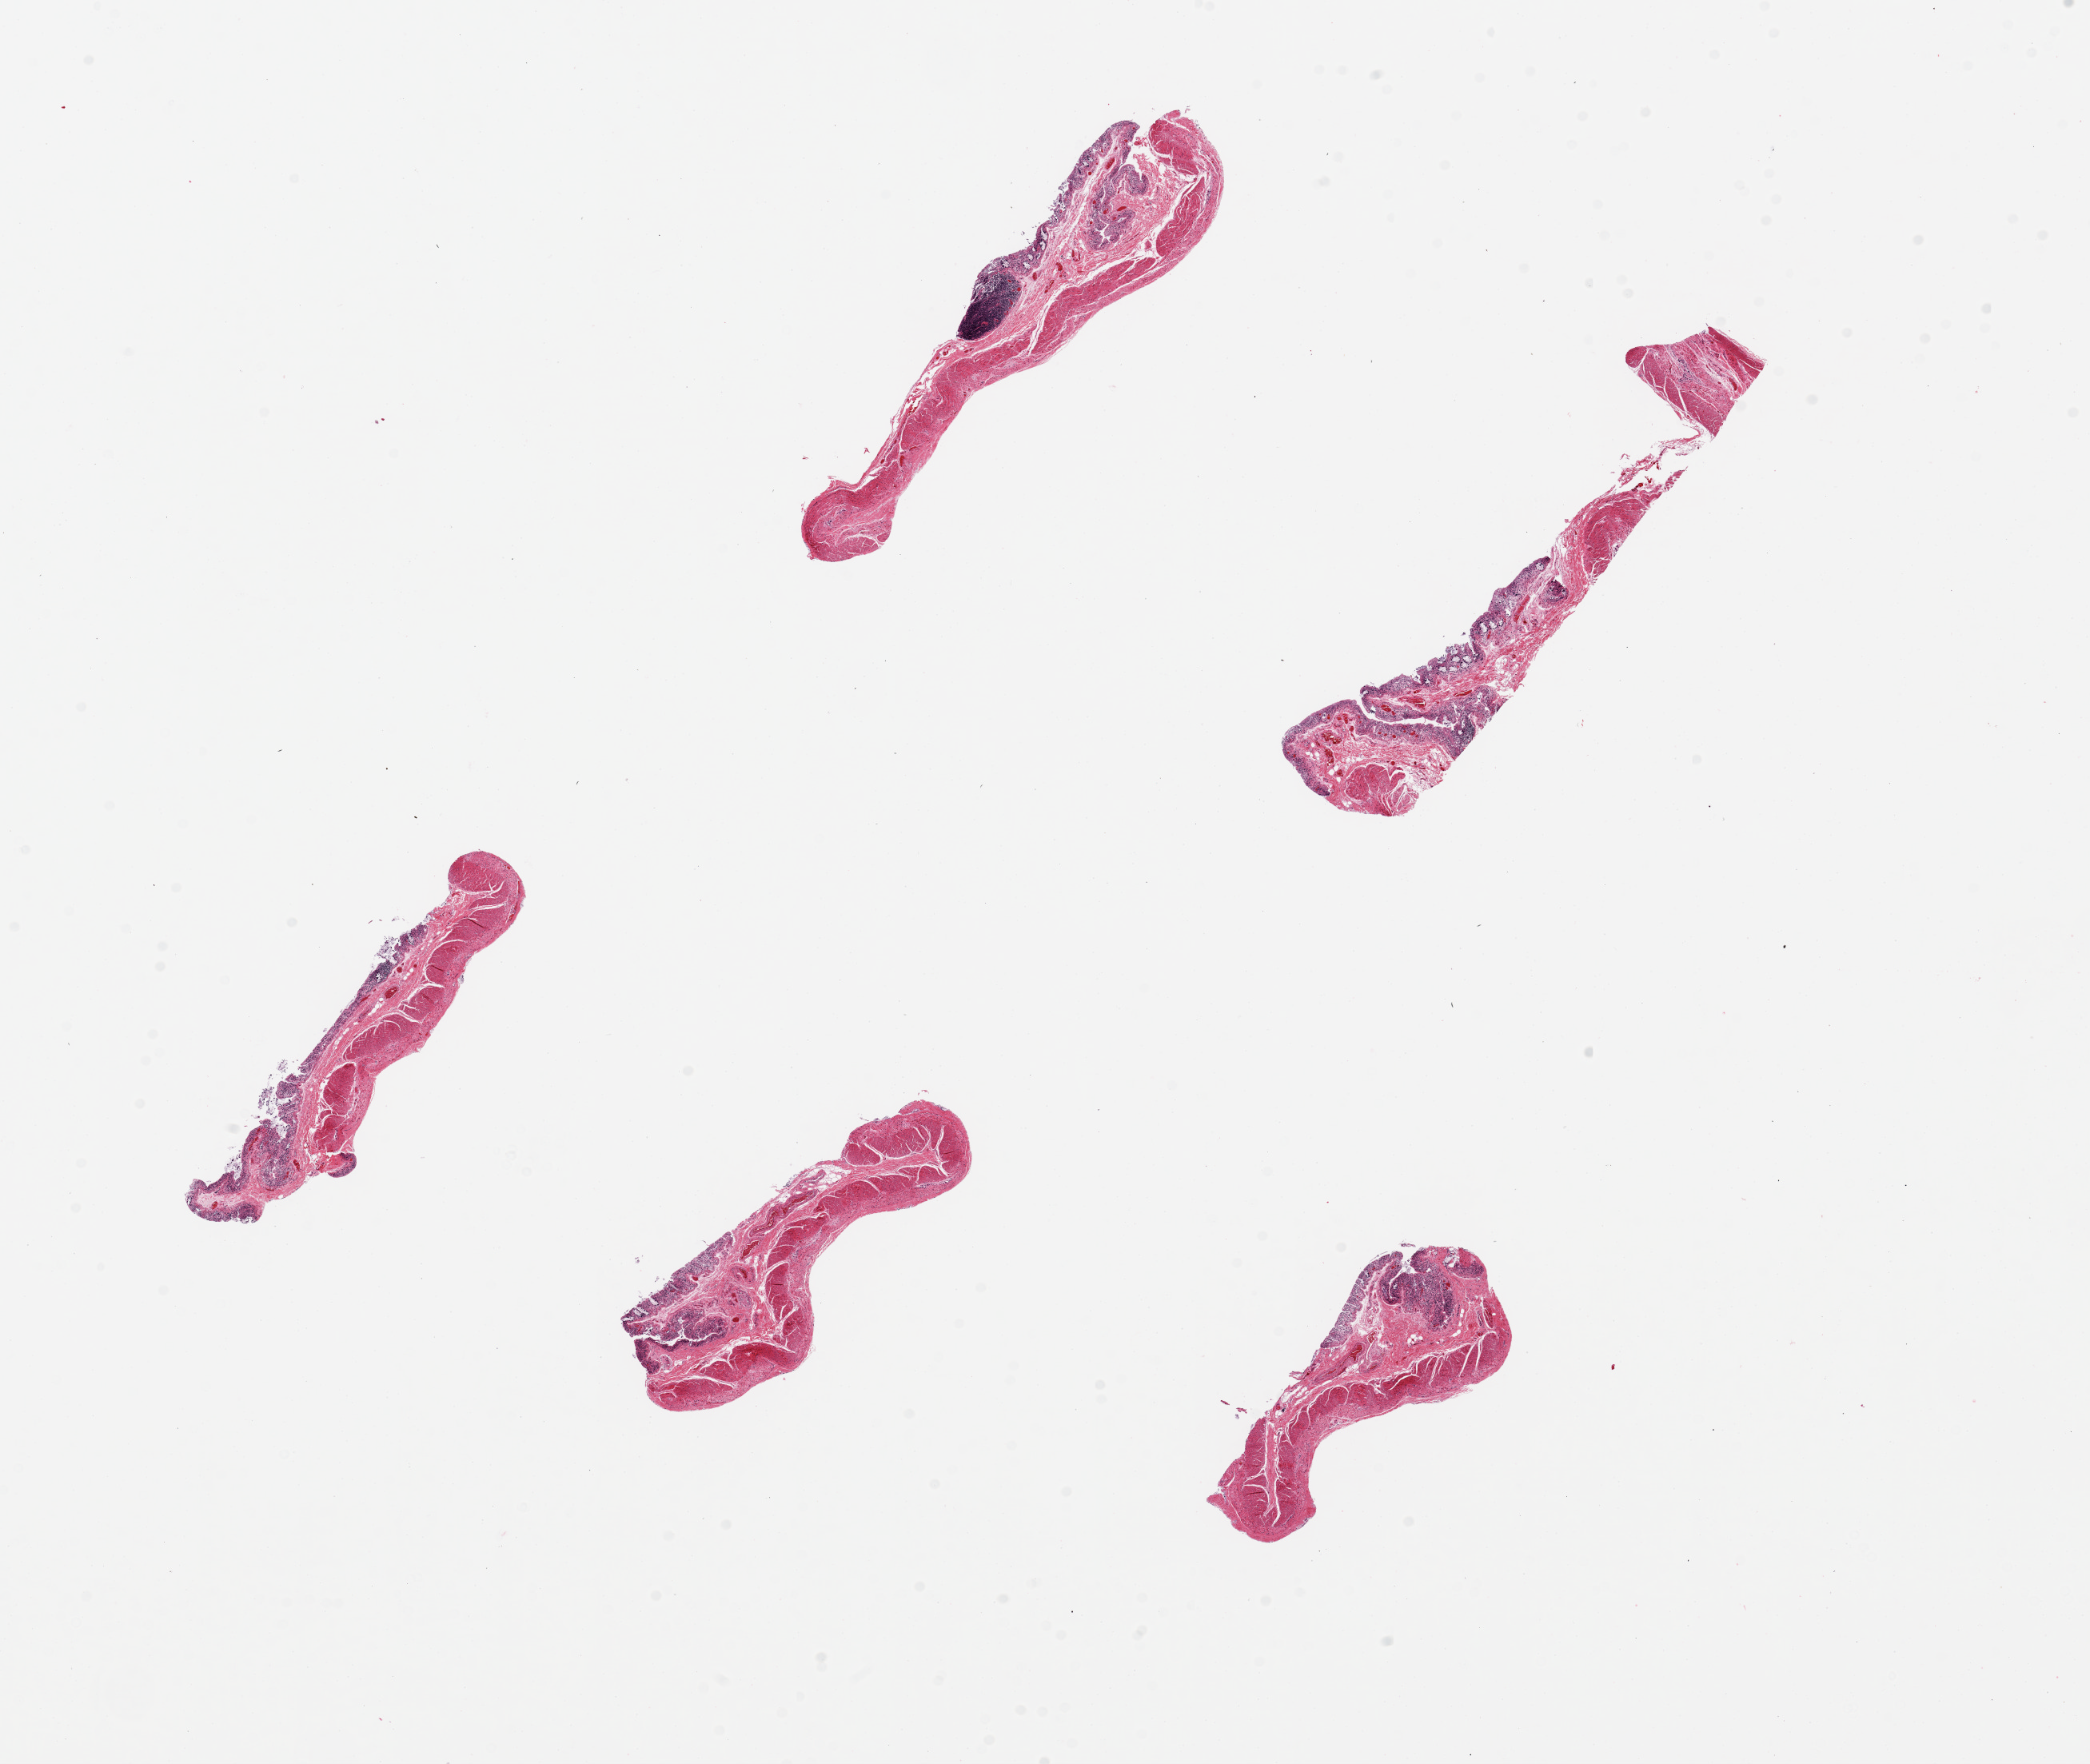
Digitized hematoxylin and eosin (H&E)-stained section — whole scanned area (about 20.7 x 17.4 mm) shown as a low-resolution overview, PAXgene-fixed, paraffin-embedded tissue, sampled site (target tissue): transverse colon, donor tissue sample. Donor: male.
• pathologist's review note for this sample: 6 pieces, up to 6x1mm; mucosa=3; muscle=2